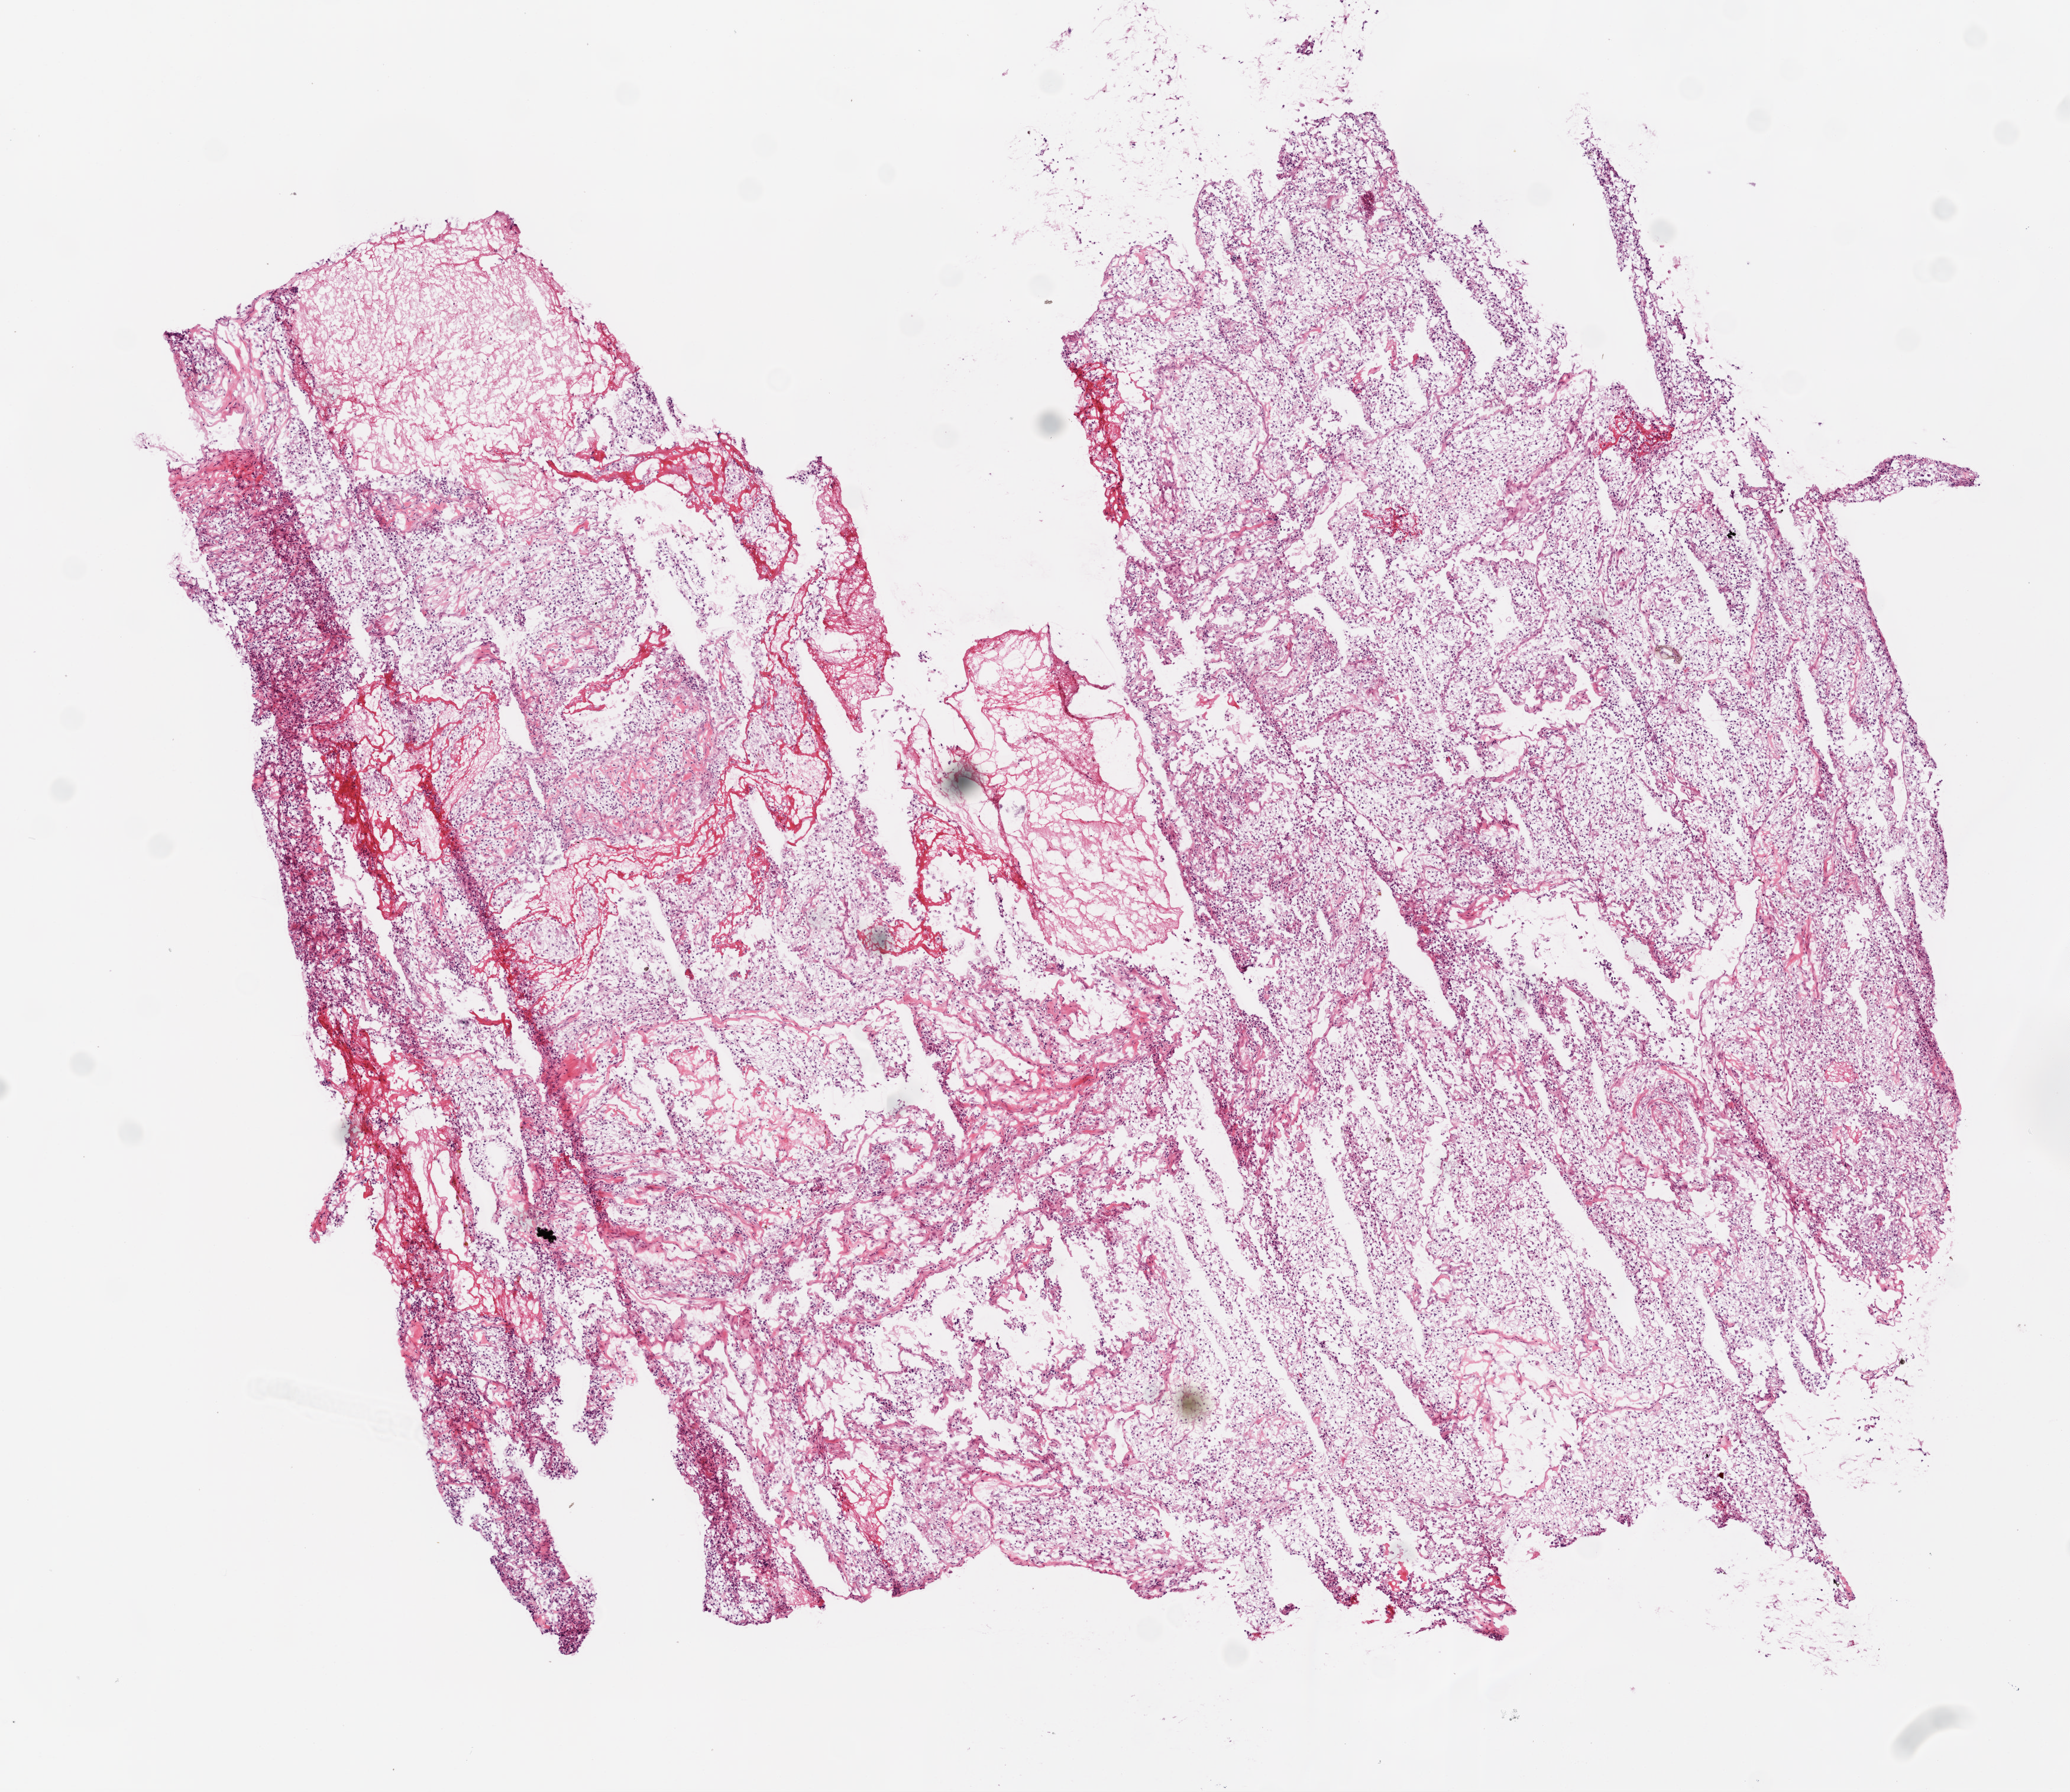
Whole-slide histology image, H&E, shown as a low-resolution overview of the whole scanned area (about 7.0 x 6.1 mm, slide scanned at 20x); frozen section from the top of the tissue portion; kidney, primary tumour sample. Patient: female, age at initial diagnosis 70 years. Histologic grade: G2 (moderately differentiated). Composition of this section per pathologist review: tumour cells 85%, tumour nuclei 85%, normal cells 0%, stromal cells 15%, necrosis 0%.
AJCC pathologic stage: III. TNM: T3a N0 M0. Lymph nodes positive (case pathology): 0 of 2 examined. Diagnosis: Clear cell adenocarcinoma, NOS.